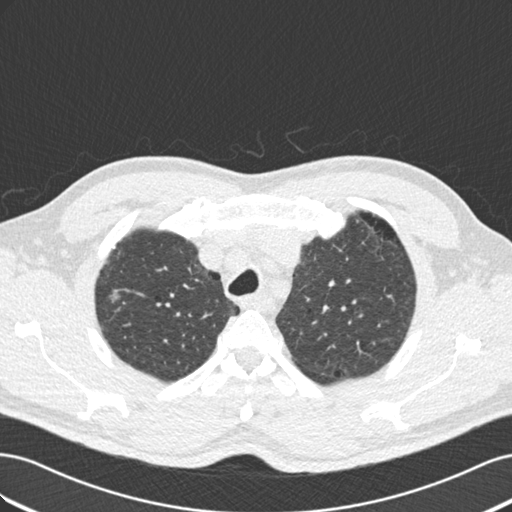
Low-dose screening chest CT, one axial slice. Position 147 of 187 along the scan axis. Reconstruction kernel B30f. 120 kVp. Lung window (W 1500 / L -600 HU). 512 × 512 image matrix, field of view 360 × 360 mm.
Annotated regions visible in this slice (manually delineated by an expert):
- lesion 1 (tumor, upper lobe of right lung): bounding box (x1, y1, x2, y2) in pixels: (110, 292, 120, 303)